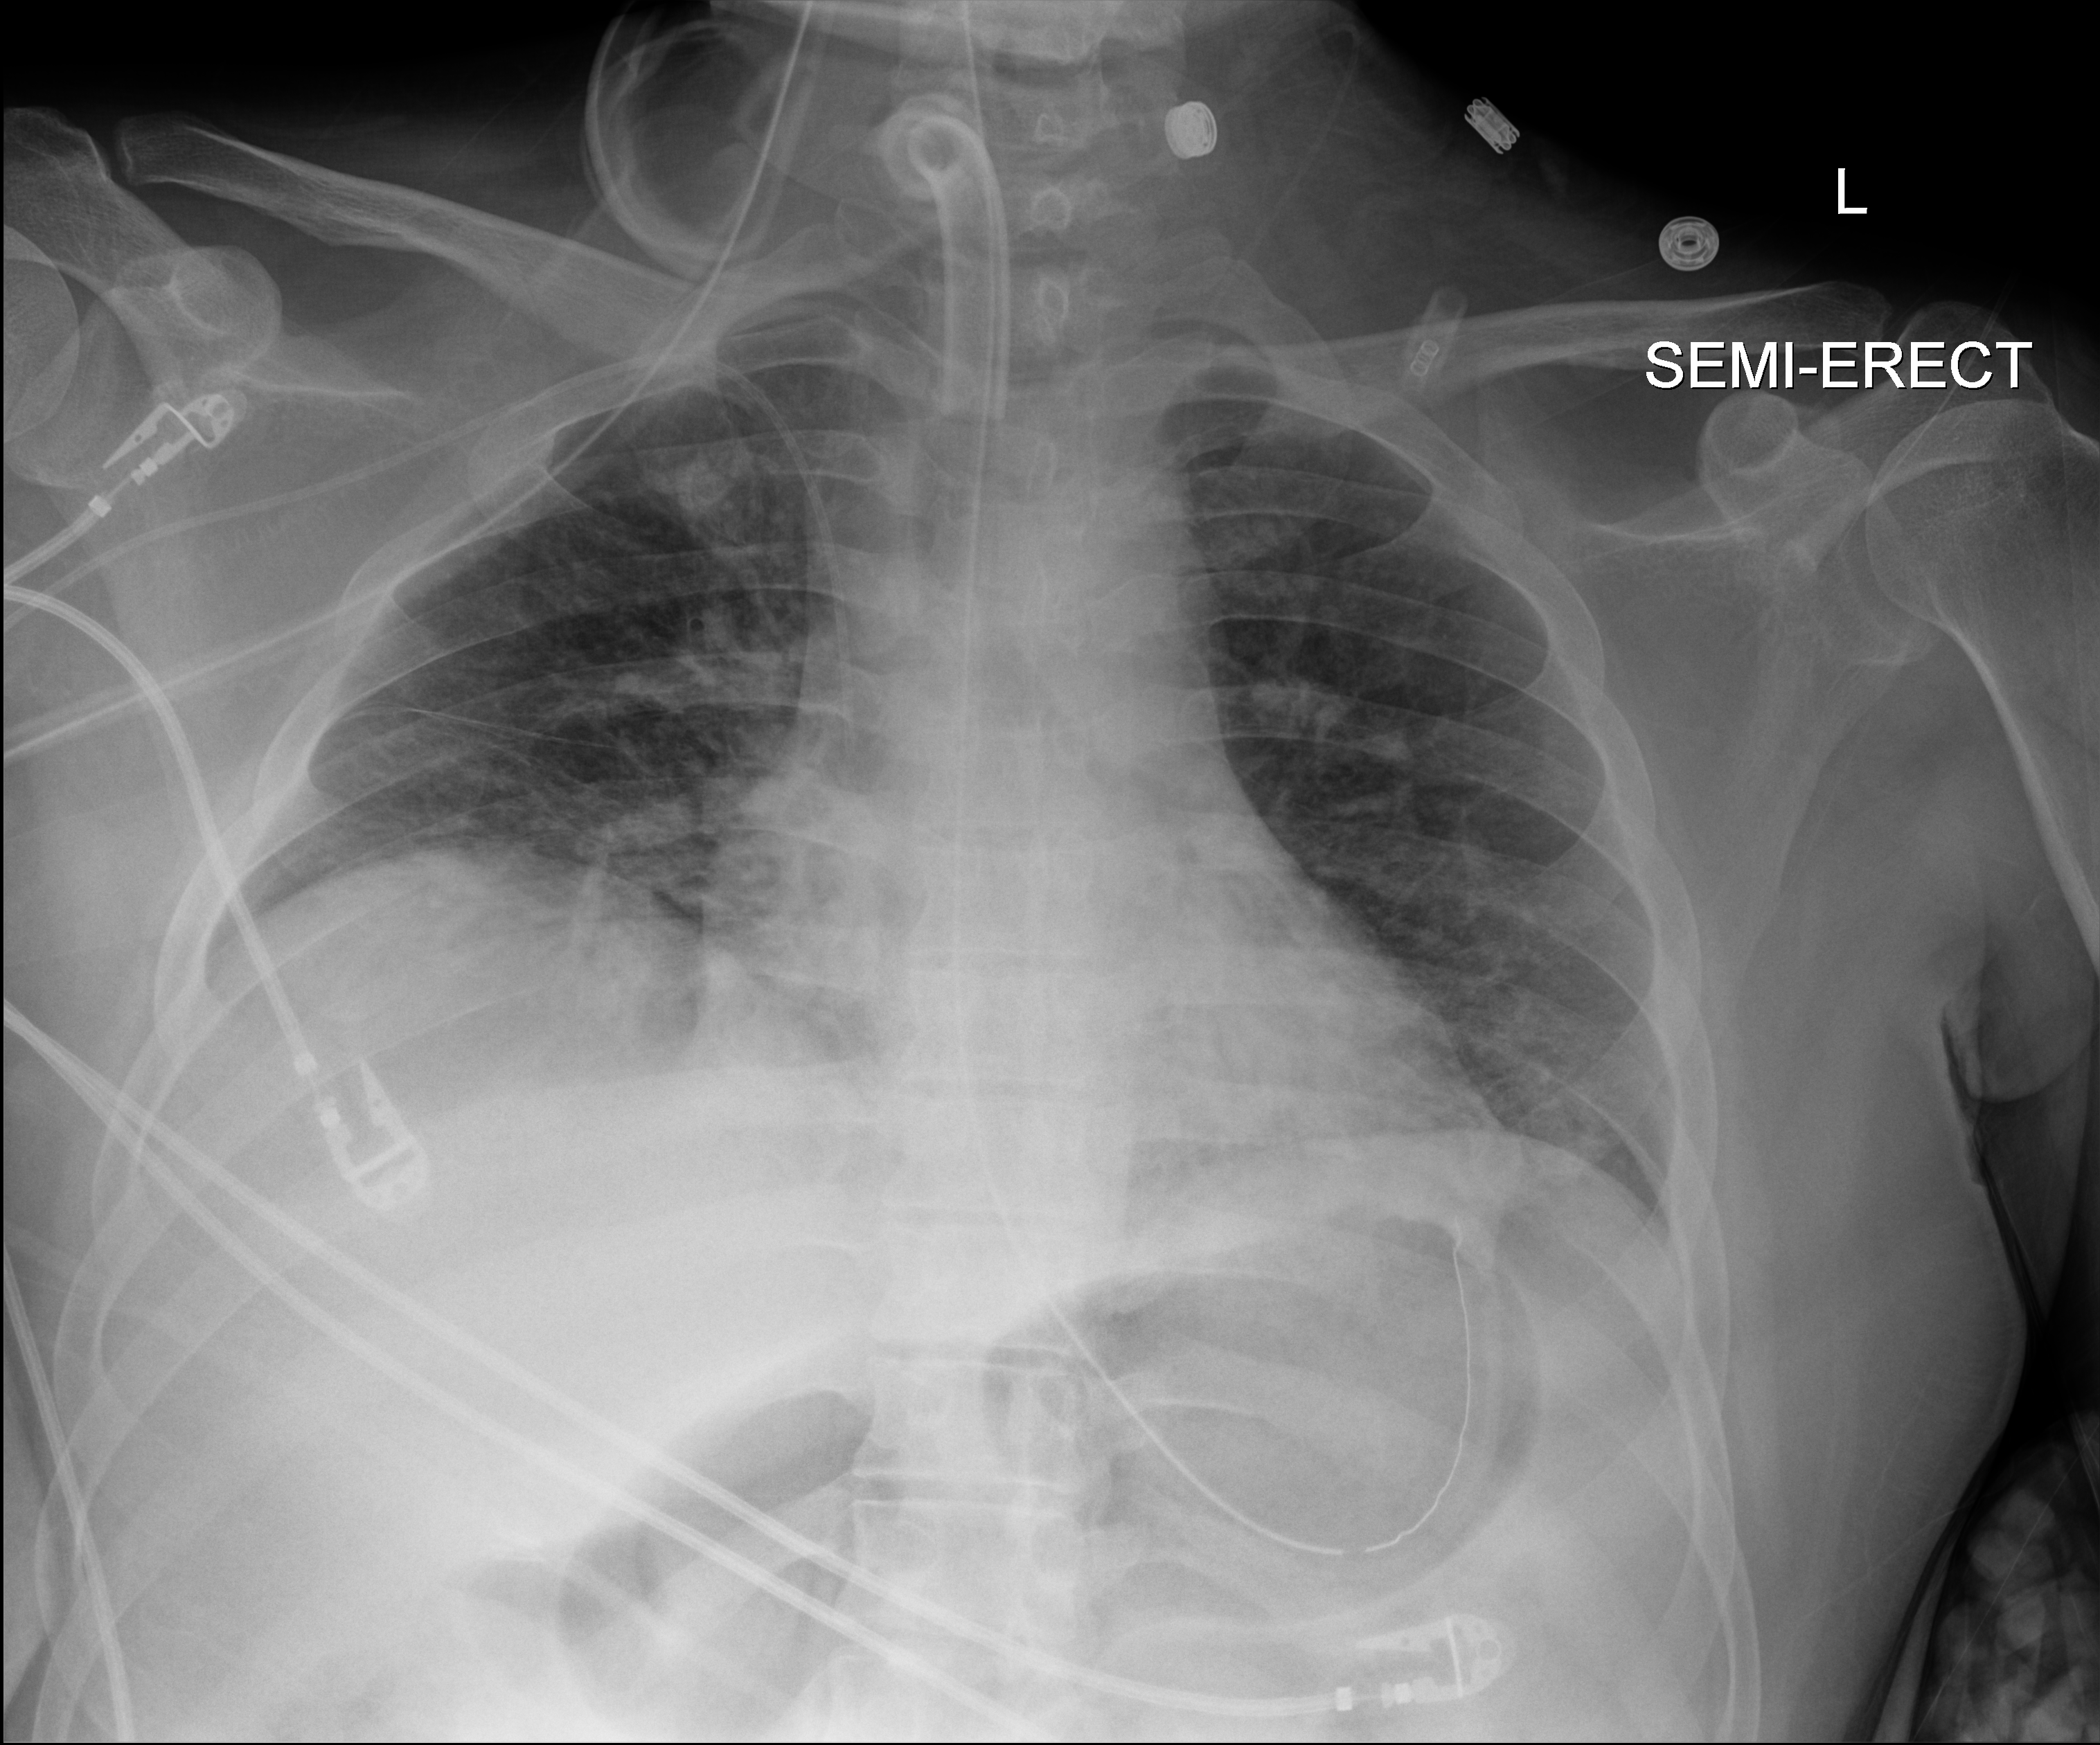
Bedside chest radiograph (digital radiography), anteroposterior (AP) projection. Patient hospitalised with COVID-19; male, aged 18–59 years.
Admission-level facts for this patient (not findings on this image; timing relative to this image not recorded):
- admitted to intensive care during this hospital stay: yes